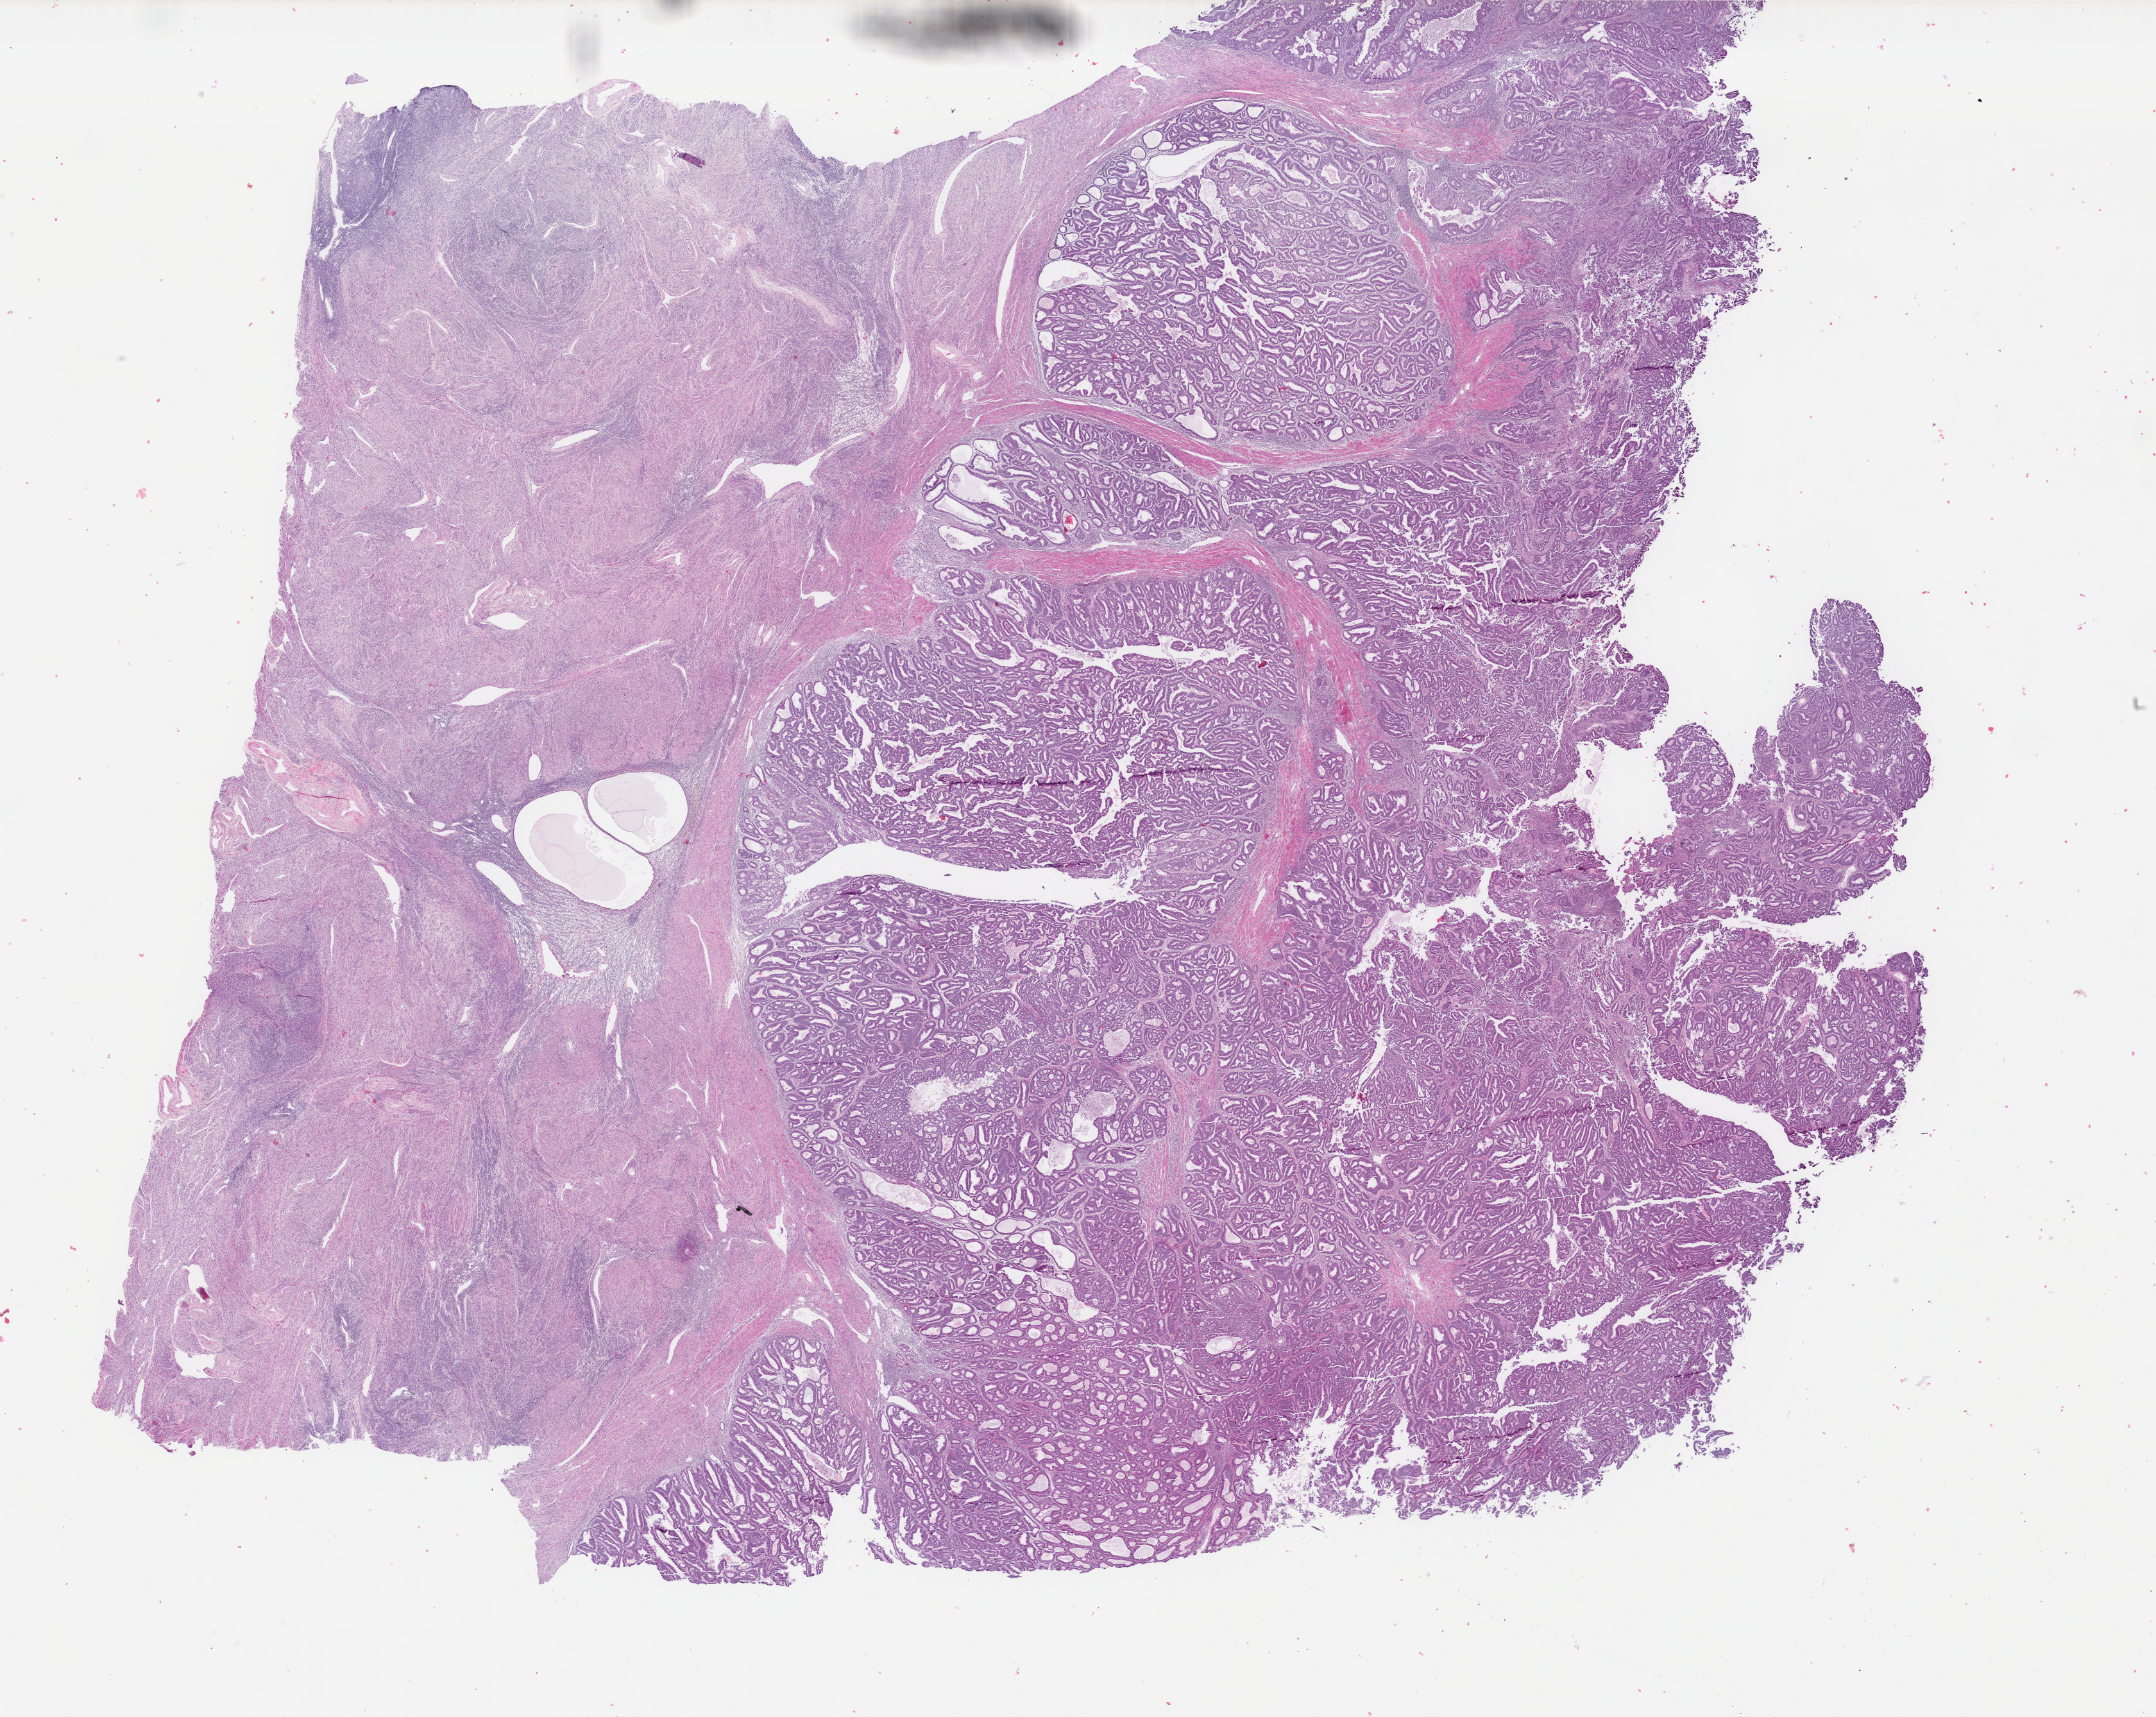
Whole-slide histology image, Hematoxylin and eosin (H&E) stained — a low-resolution overview of the entire scanned area, about 26.7 x 21.2 mm (from a 40x scan). Formalin-fixed paraffin-embedded (FFPE) diagnostic section. Sample: primary tumour, uterus. Patient: female, age at initial diagnosis 63 years. Histologic grade: G2 (moderately differentiated).
FIGO stage: IA. Diagnosis: Endometrioid adenocarcinoma, NOS (endometrium).